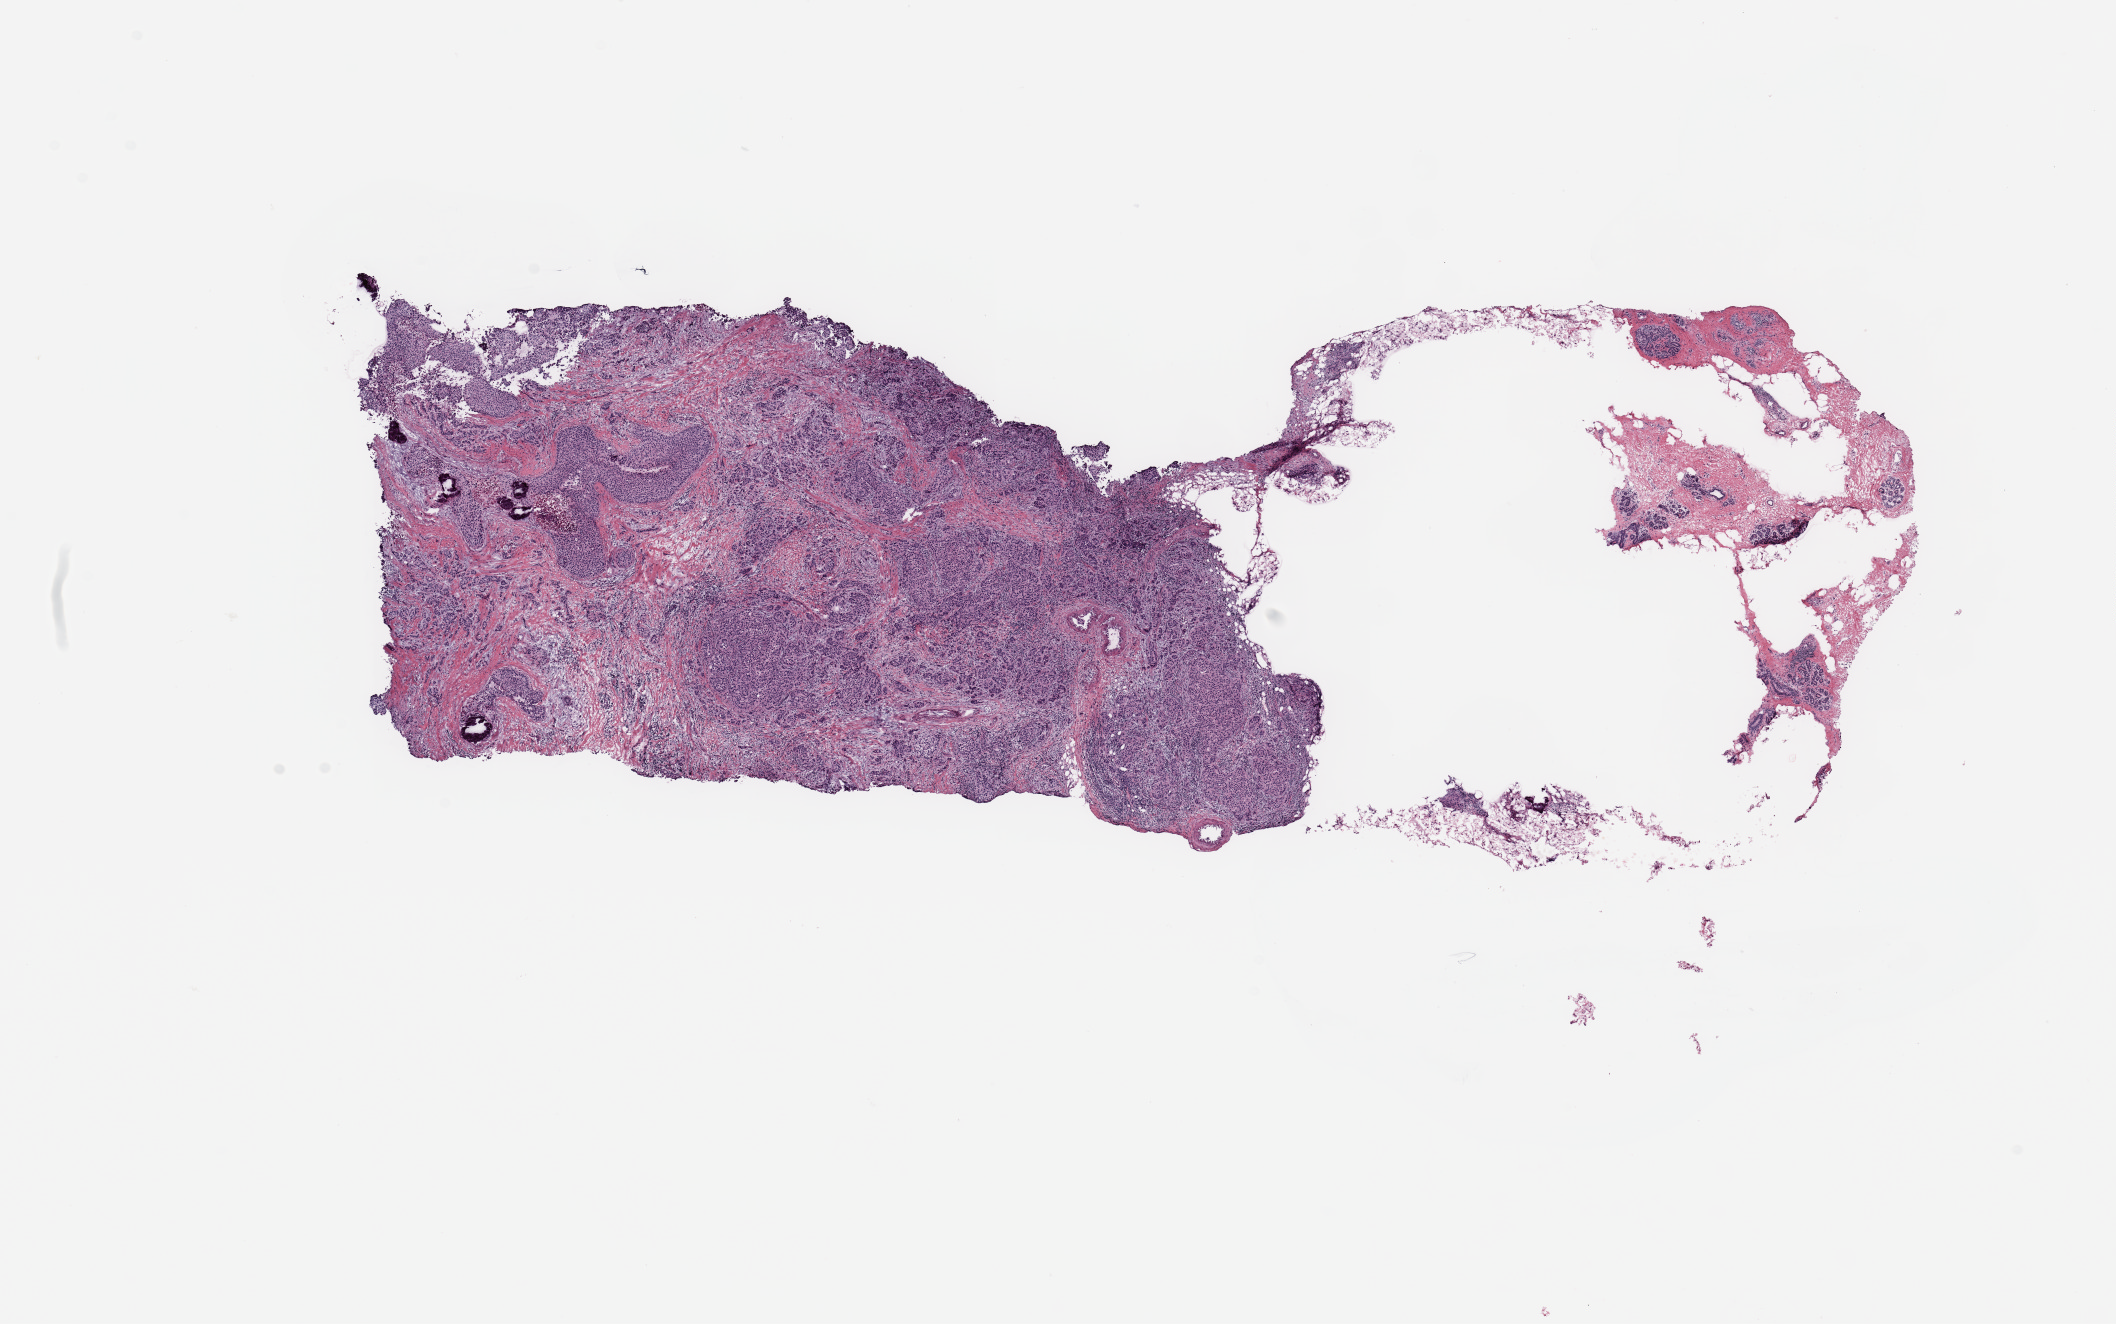
Digitized Hematoxylin and eosin (H&E) stained tissue section (whole slide) — low-resolution overview of the scanned area, about 16.7 x 10.5 mm; breast, tissue type not recorded.
Patient diagnosis (cohort enrolment): breast cancer (breast).